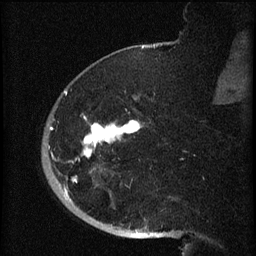
Breast MRI (dynamic contrast-enhanced), one sagittal slice. Slice 16 of 60 in the series (ordered by position). Dynamic contrast-enhanced series, image 2 of 3 at this slice position (ordered by acquisition). 1.5 T. TE 4.2 ms, TR 8.2 ms. 2 mm slice thickness. 256 × 256 image matrix, field of view 180 × 180 mm. Patient: female, 71 years.
Annotated regions visible in this slice (semi-automatically segmented with operator editing):
- analysis volume of interest (the breast-tissue region the enhancement analysis was run in; not a lesion): bounding box (x1, y1, x2, y2) in pixels: (42, 72, 145, 196)
- tumour enhancement mask (voxels above the 70 % enhancement threshold inside the analysis volume of interest): (50, 91, 141, 195)